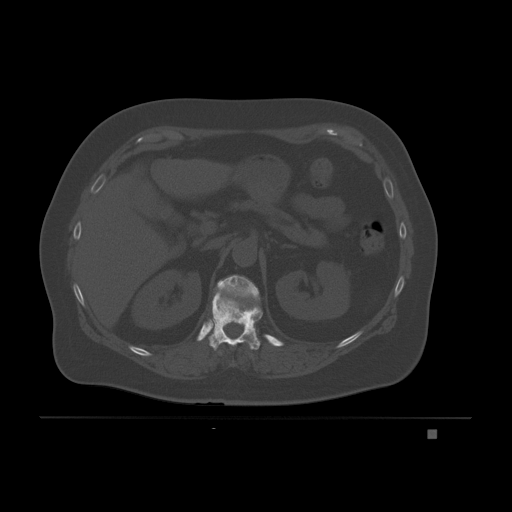
CT including the spine, one axial slice. Slice 89 of 221 in the series (ordered by position). Bone window (W 1800 / L 400 HU). 512 × 512 image matrix, field of view 474 × 474 mm. Female patient, age 63 years. From the clinical record (not read from this slice): primary cancer: breast.
Structures marked on this image (semi-automatic segmentation, software-assisted and operator-edited):
- T11 vertebra: bounding box <209,289,263,351> (left, top, right, bottom; pixels)
- T12 vertebra: <216,275,260,298>